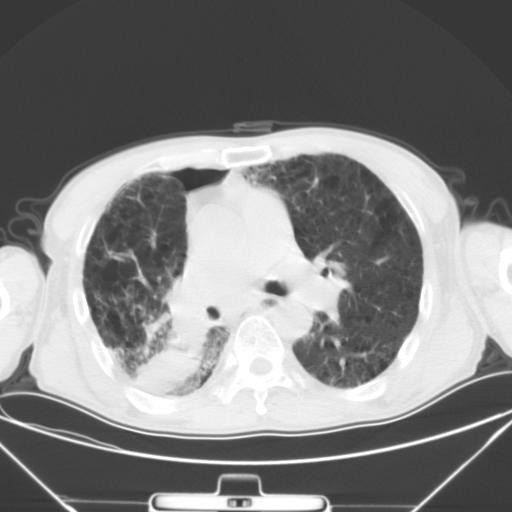
Chest CT, one axial slice. Position 27 of 50 along the scan axis. 120 kVp. Lung window (W 1500 / L -600 HU). 512 × 512 image matrix, field of view 373 × 373 mm. Patient: male, 65 years. Case-level facts recorded for this patient, not image findings: clinical TNM (as recorded): T3 N1 M1a.
Structures marked on this image (rectangle marked by the reading radiologist):
- lung tumour (recorded histology: squamous cell carcinoma): box from (x=119, y=306) to (x=215, y=412) px